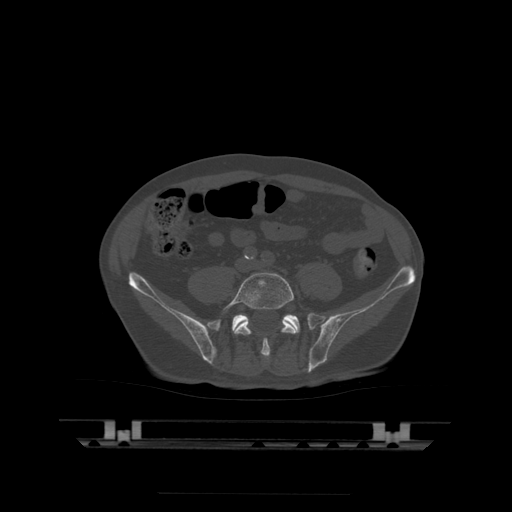
CT including the spine, one axial slice. Position 68 of 522 along the scan axis. Bone window (W 1800 / L 400 HU). 1.25 mm slice thickness. 512 × 512 image matrix, field of view 436 × 436 mm. Patient age 68 years. From the clinical record (not read from this slice): primary cancer: urothelial.
Structures marked on this image (semi-automatic segmentation, software-assisted and operator-edited):
- L5 vertebra: bounding box (x1, y1, x2, y2) in pixels: (224, 273, 297, 360)